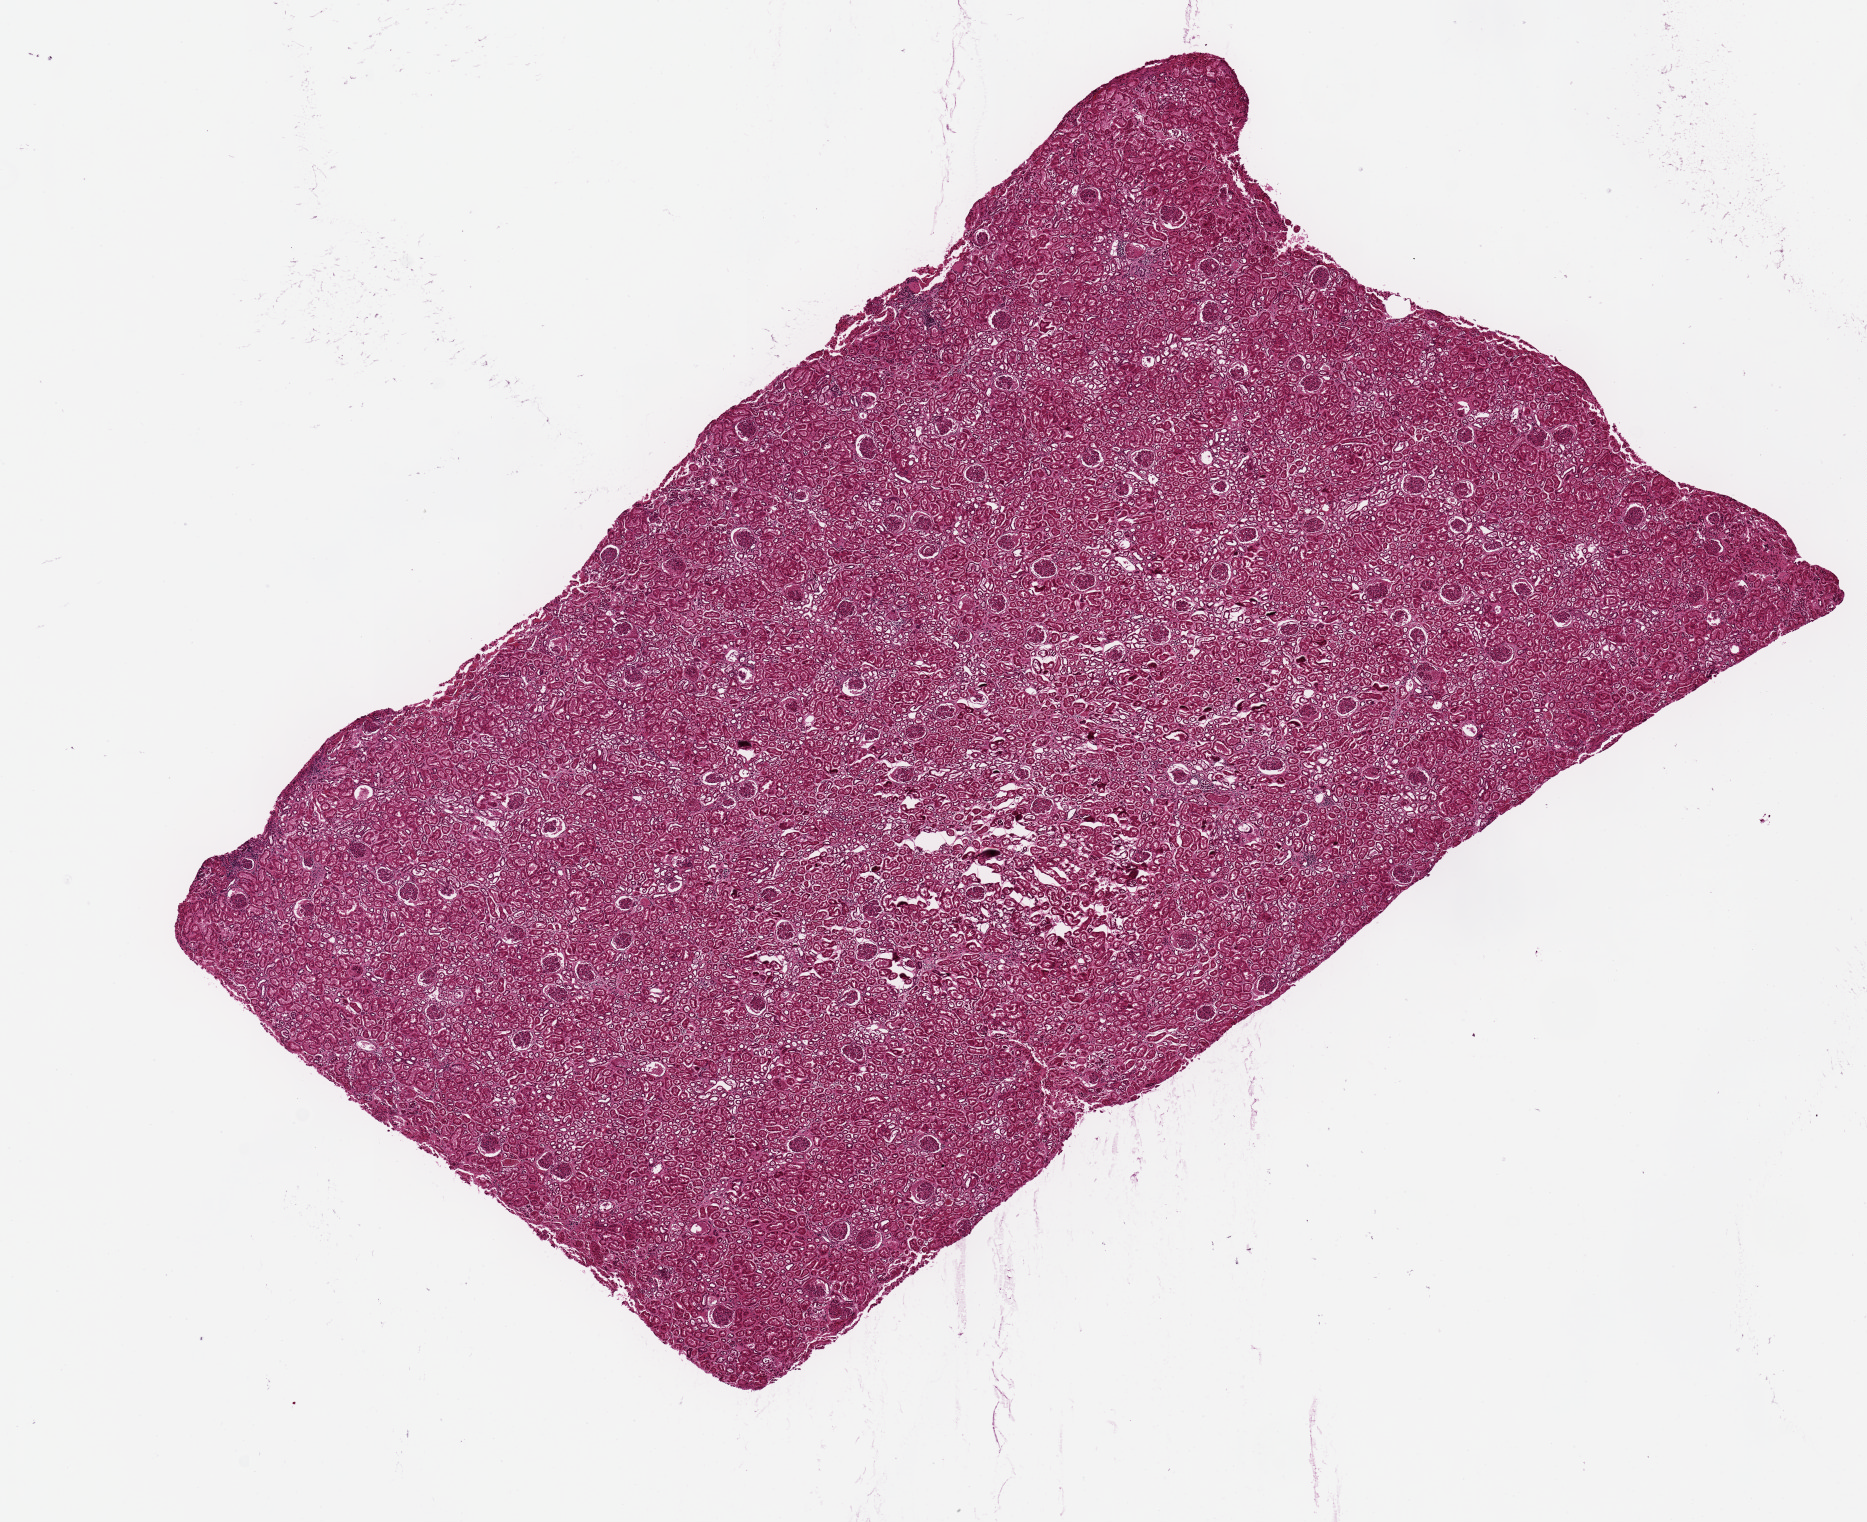
H&E whole-slide image, a low-resolution overview of the entire scanned area, about 14.8 x 12.0 mm (acquisition: 20x scan); PAXgene-fixed paraffin-embedded (PFPE) section; sampled site (target tissue): renal cortex; donor tissue sample. Donor: female.
Reviewer comment on this tissue sample: 10x6 mm; CORTICAL TISSUE not medulla.